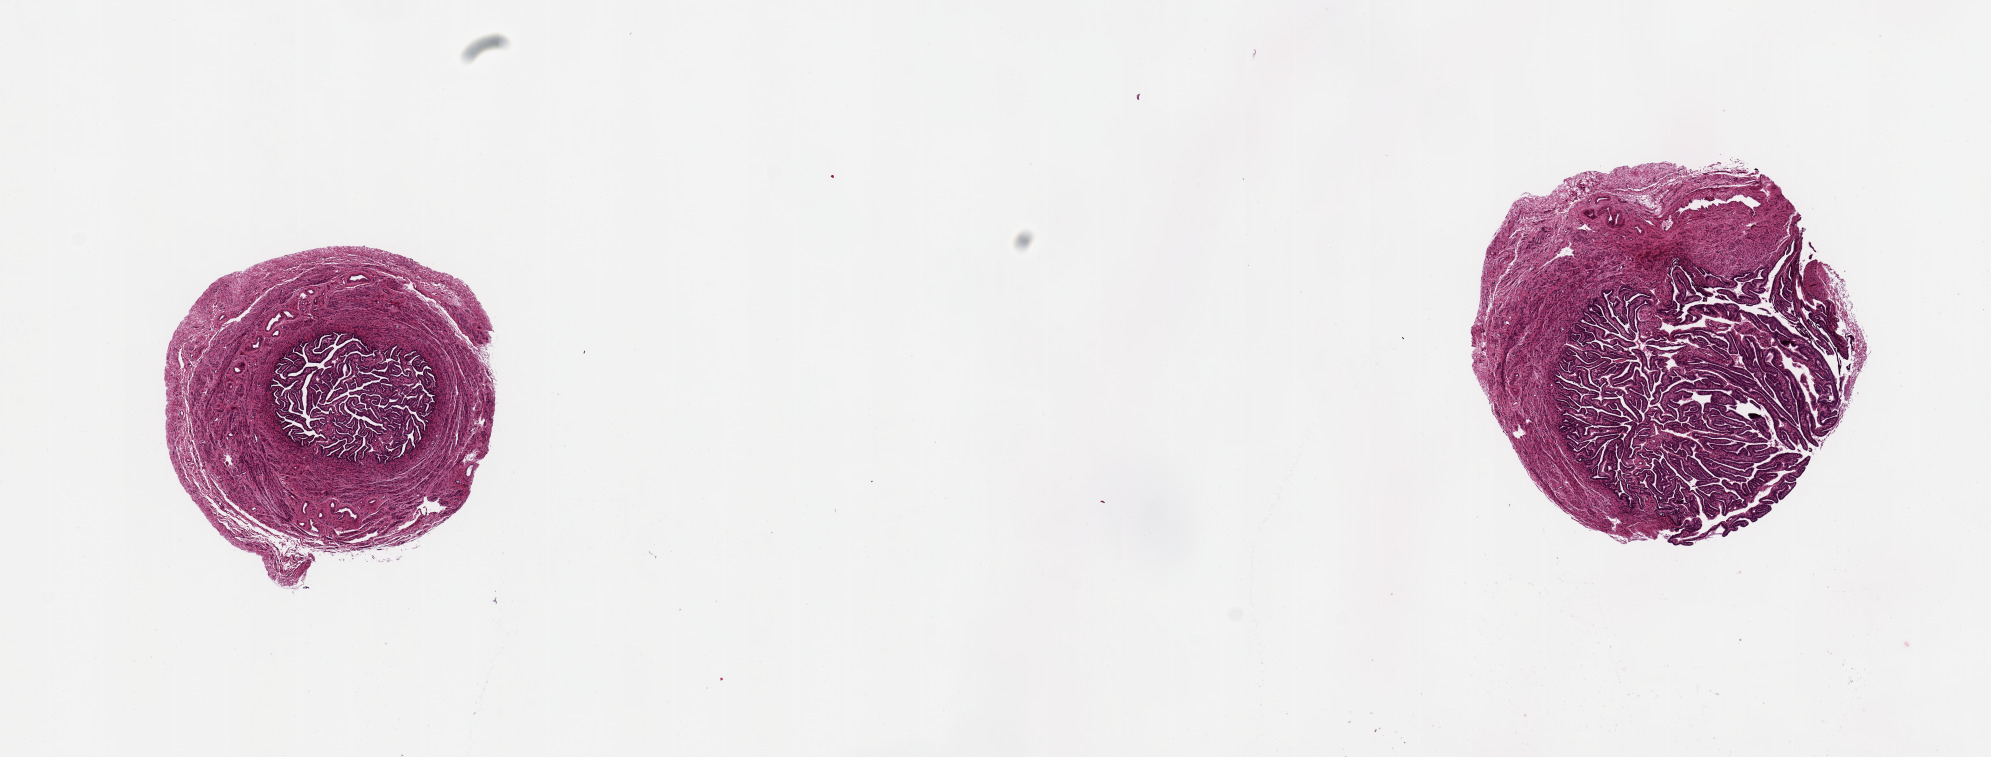
Digitized haematoxylin and eosin-stained section, brightfield — a low-resolution overview of the entire scanned area, about 15.8 x 6.0 mm (acquisition: 20x scan); PAXgene-fixed, paraffin-embedded tissue; section of fallopian tube (target tissue); tissue donor sample.
Reviewer comment on this tissue sample: 2 ~2.5mm pieces. Epithelium well preserved.